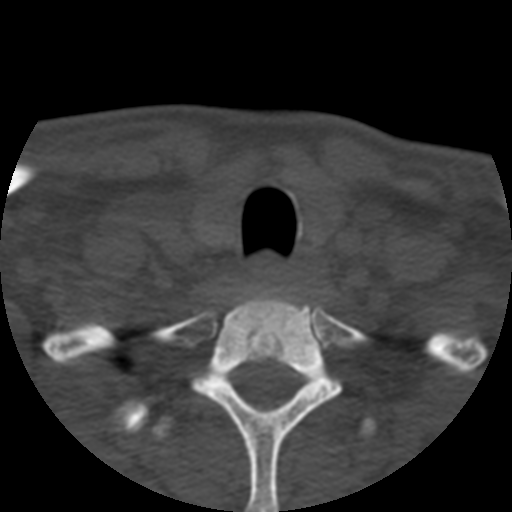
CT including the spine, one axial slice; reconstruction kernel STANDARD; 120 kVp; bone window (W 1800 / L 400 HU); 1.25 mm slice thickness; 512 × 512 image matrix. Patient age 57 years. Case-level facts recorded for this patient, not image findings: primary cancer: prostate.
Annotated regions visible in this slice (semi-automatic segmentation, software-assisted and operator-edited):
- T1 vertebra: bounding box (x1, y1, x2, y2) in pixels: (163, 286, 385, 512)
- T2 vertebra: (150, 411, 383, 447)